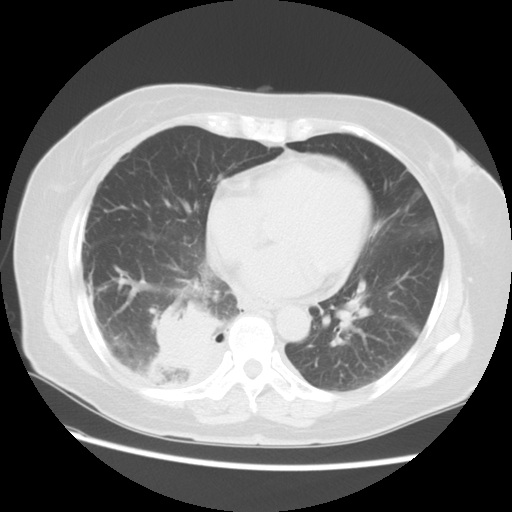
Chest CT, one axial slice. Slice 26 of 57 in the series (ordered by position). Reconstruction kernel STANDARD. 120 kVp. Lung window (W 1500 / L -600 HU). 5 mm slice thickness. 512 × 512 image matrix, field of view 350 × 350 mm. Patient: female, 69 years. Case-level facts recorded for this patient, not image findings: clinical TNM (as recorded): T2 N1 M1a.
Outlined on this slice (bounding box drawn by a radiologist):
- lung tumour (recorded histology: adenocarcinoma): bounding box [x1, y1, x2, y2] px = [145, 297, 222, 389]